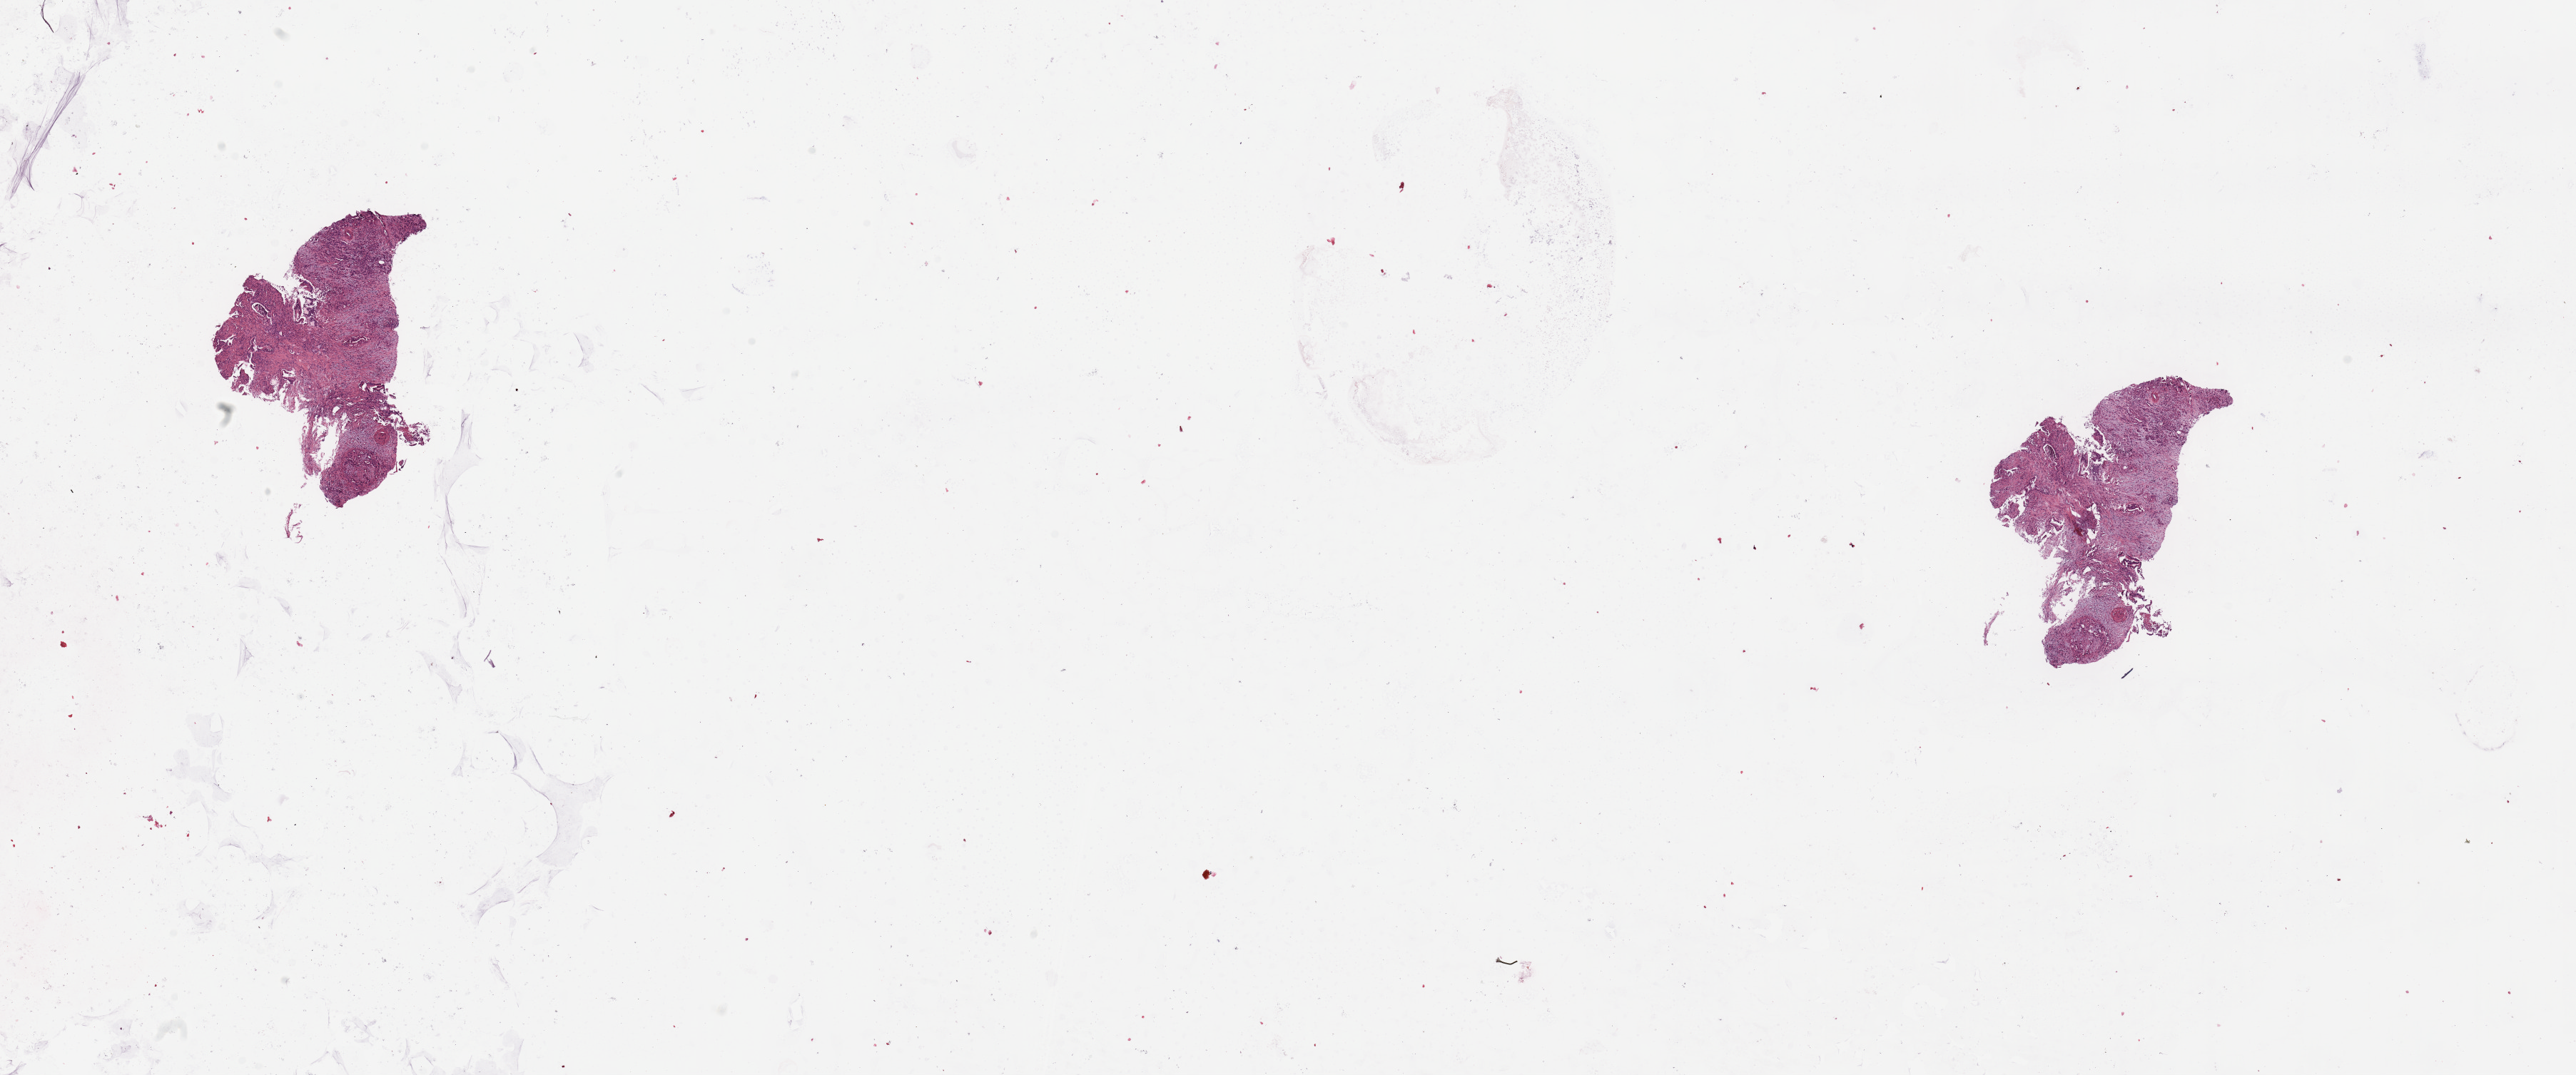
Whole-slide histology image, Hematoxylin and eosin (H&E) stained — low-resolution overview of the scanned area, about 28.5 x 11.9 mm (acquisition: 20x scan). Tumour tissue sample, pancreas. Female, 65 y/o.
- primary tumour site (as recorded): head
- patient diagnosis (cohort enrolment): ductal adenocarcinoma (pancreas)